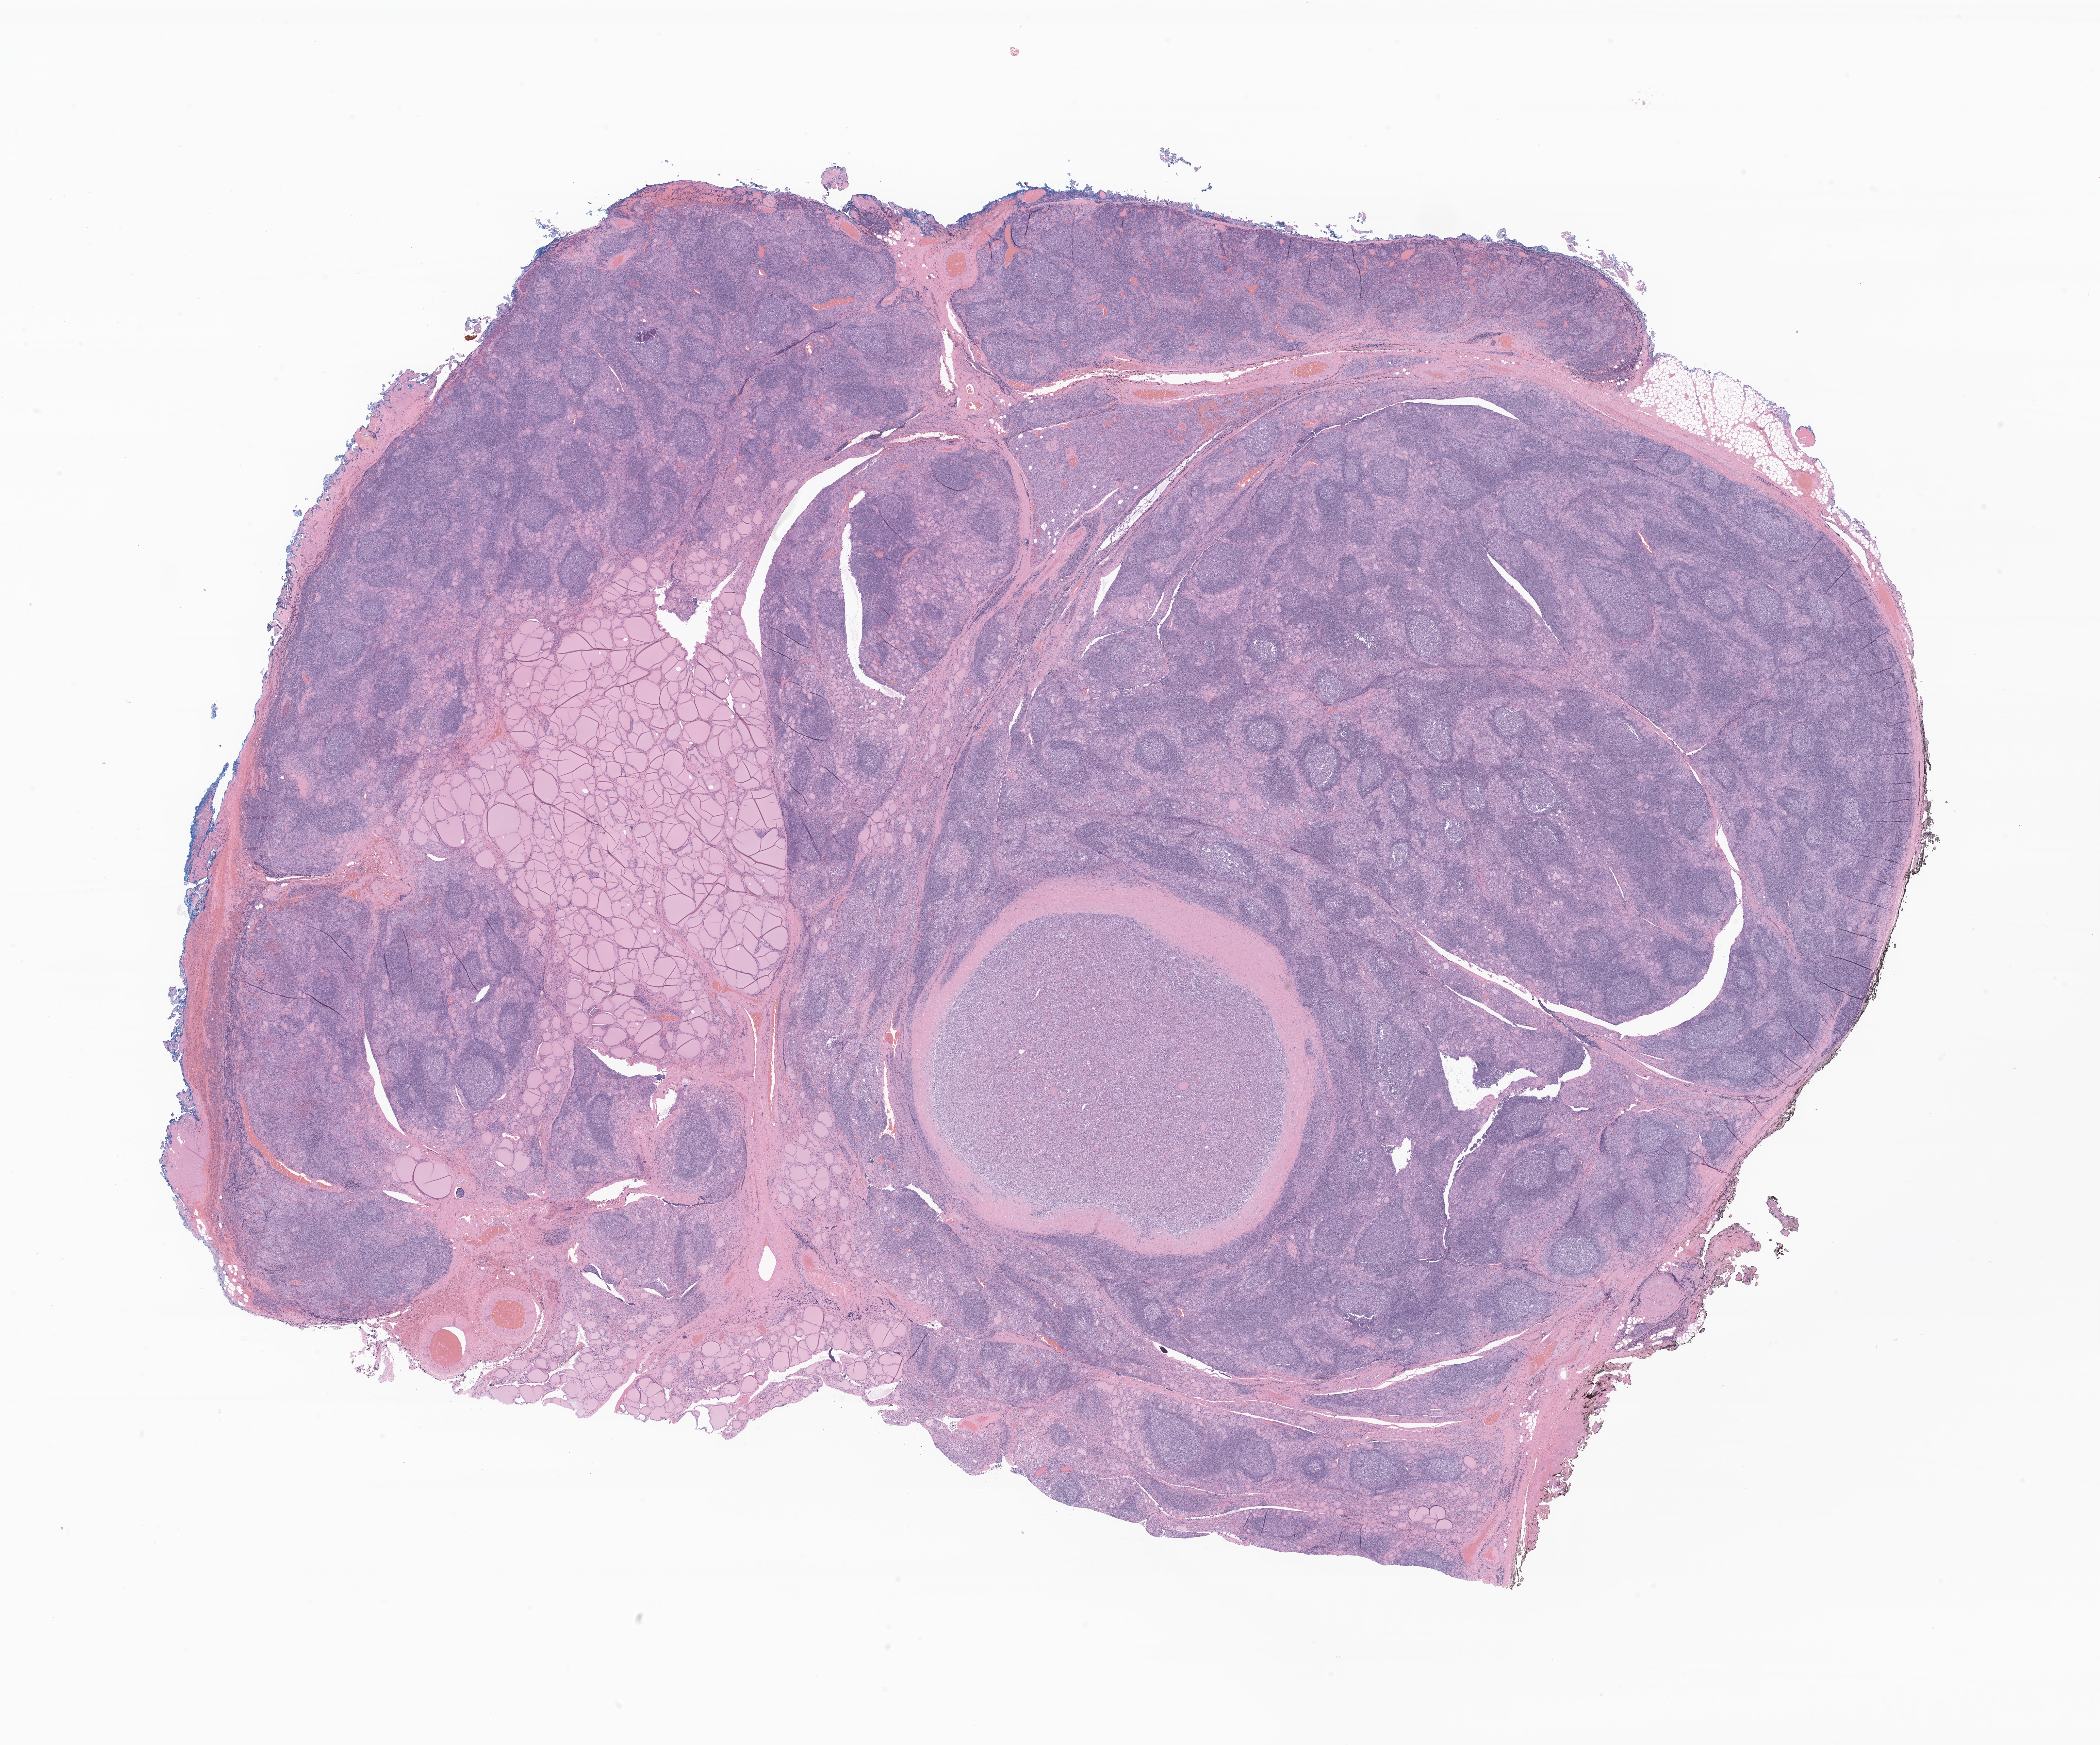
Whole-slide image, H&E stain of tumor tissue from the thyroid — a low-resolution overview of the entire scanned area, about 26.0 x 21.6 mm; formalin-fixed, paraffin-embedded (FFPE) tissue. Patient: female, age 174 months (14 years 6 months).
- diagnosis: Papillary carcinoma, NOS